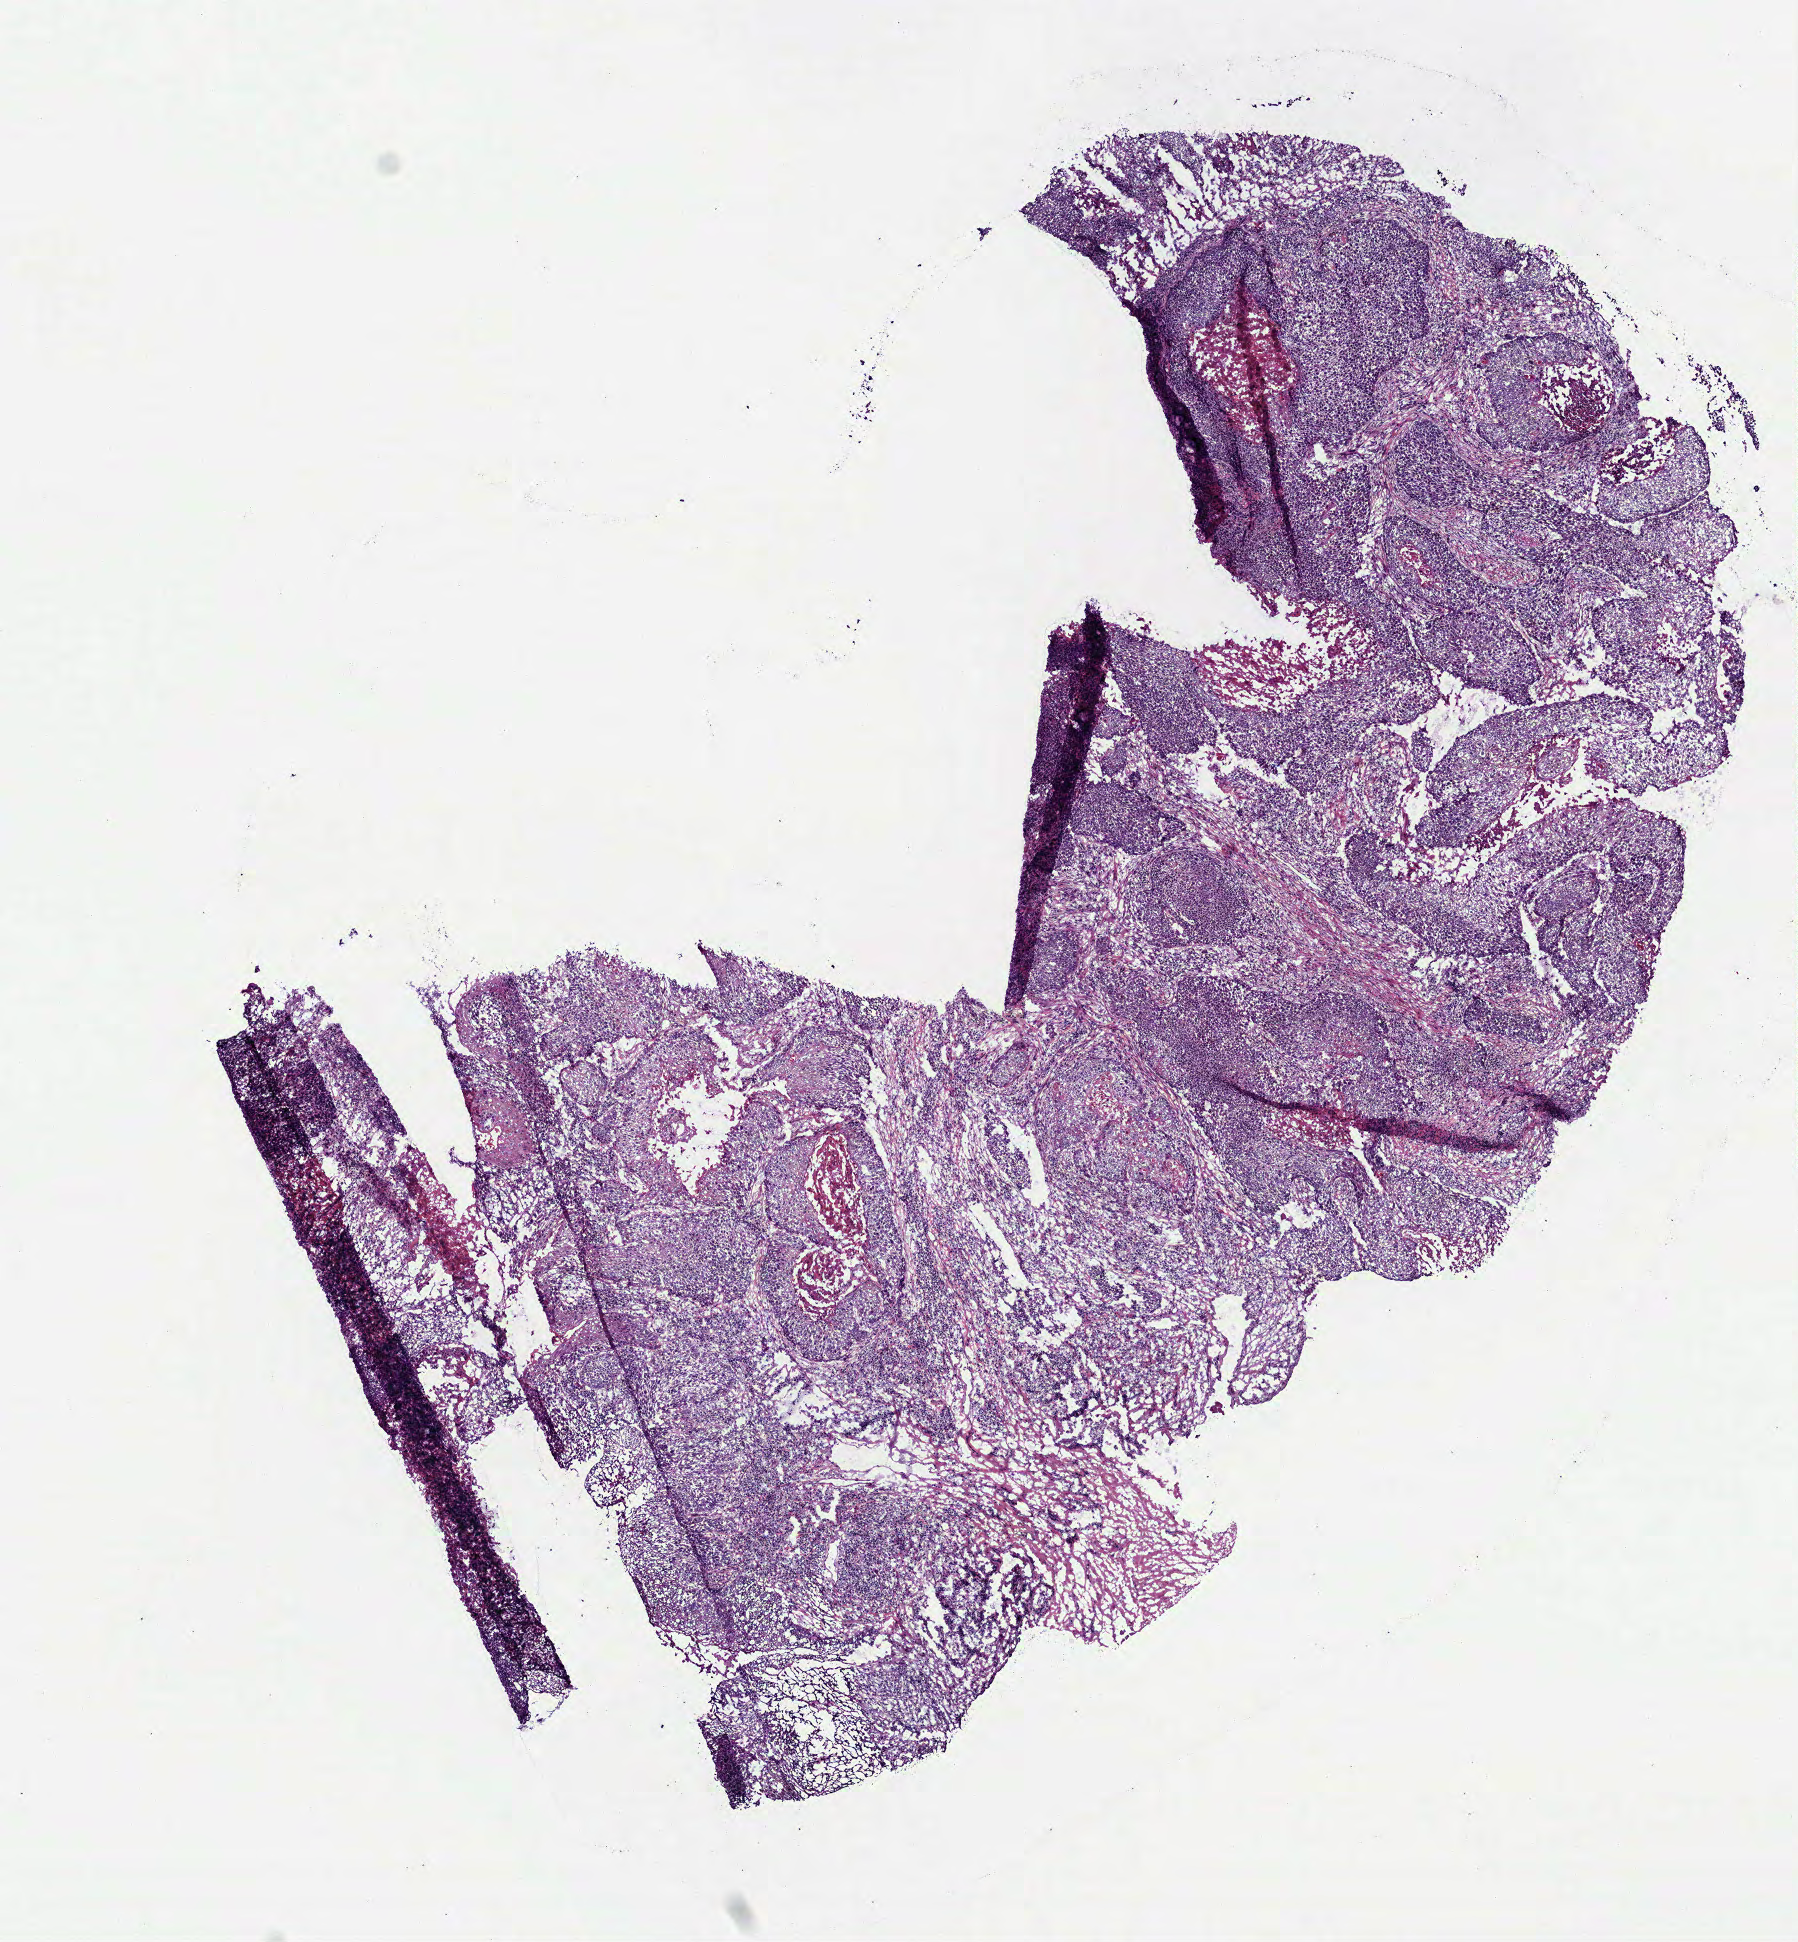
Whole-slide histology image, H&E-stained, whole scanned area (about 7.3 x 7.8 mm, from a 40x scan) shown as a low-resolution overview. Frozen section. Primary tumour sample from the head and neck. Male, age 66 years at initial diagnosis. Histologic grade: G2 (moderately differentiated). Composition of this section per pathologist review: tumour cells 77%, tumour nuclei 80%, normal cells 0%, stromal cells 15%, necrosis 8%.
TNM: T3 N2c. AJCC pathologic stage: IVA. Diagnosis: Squamous cell carcinoma, NOS.